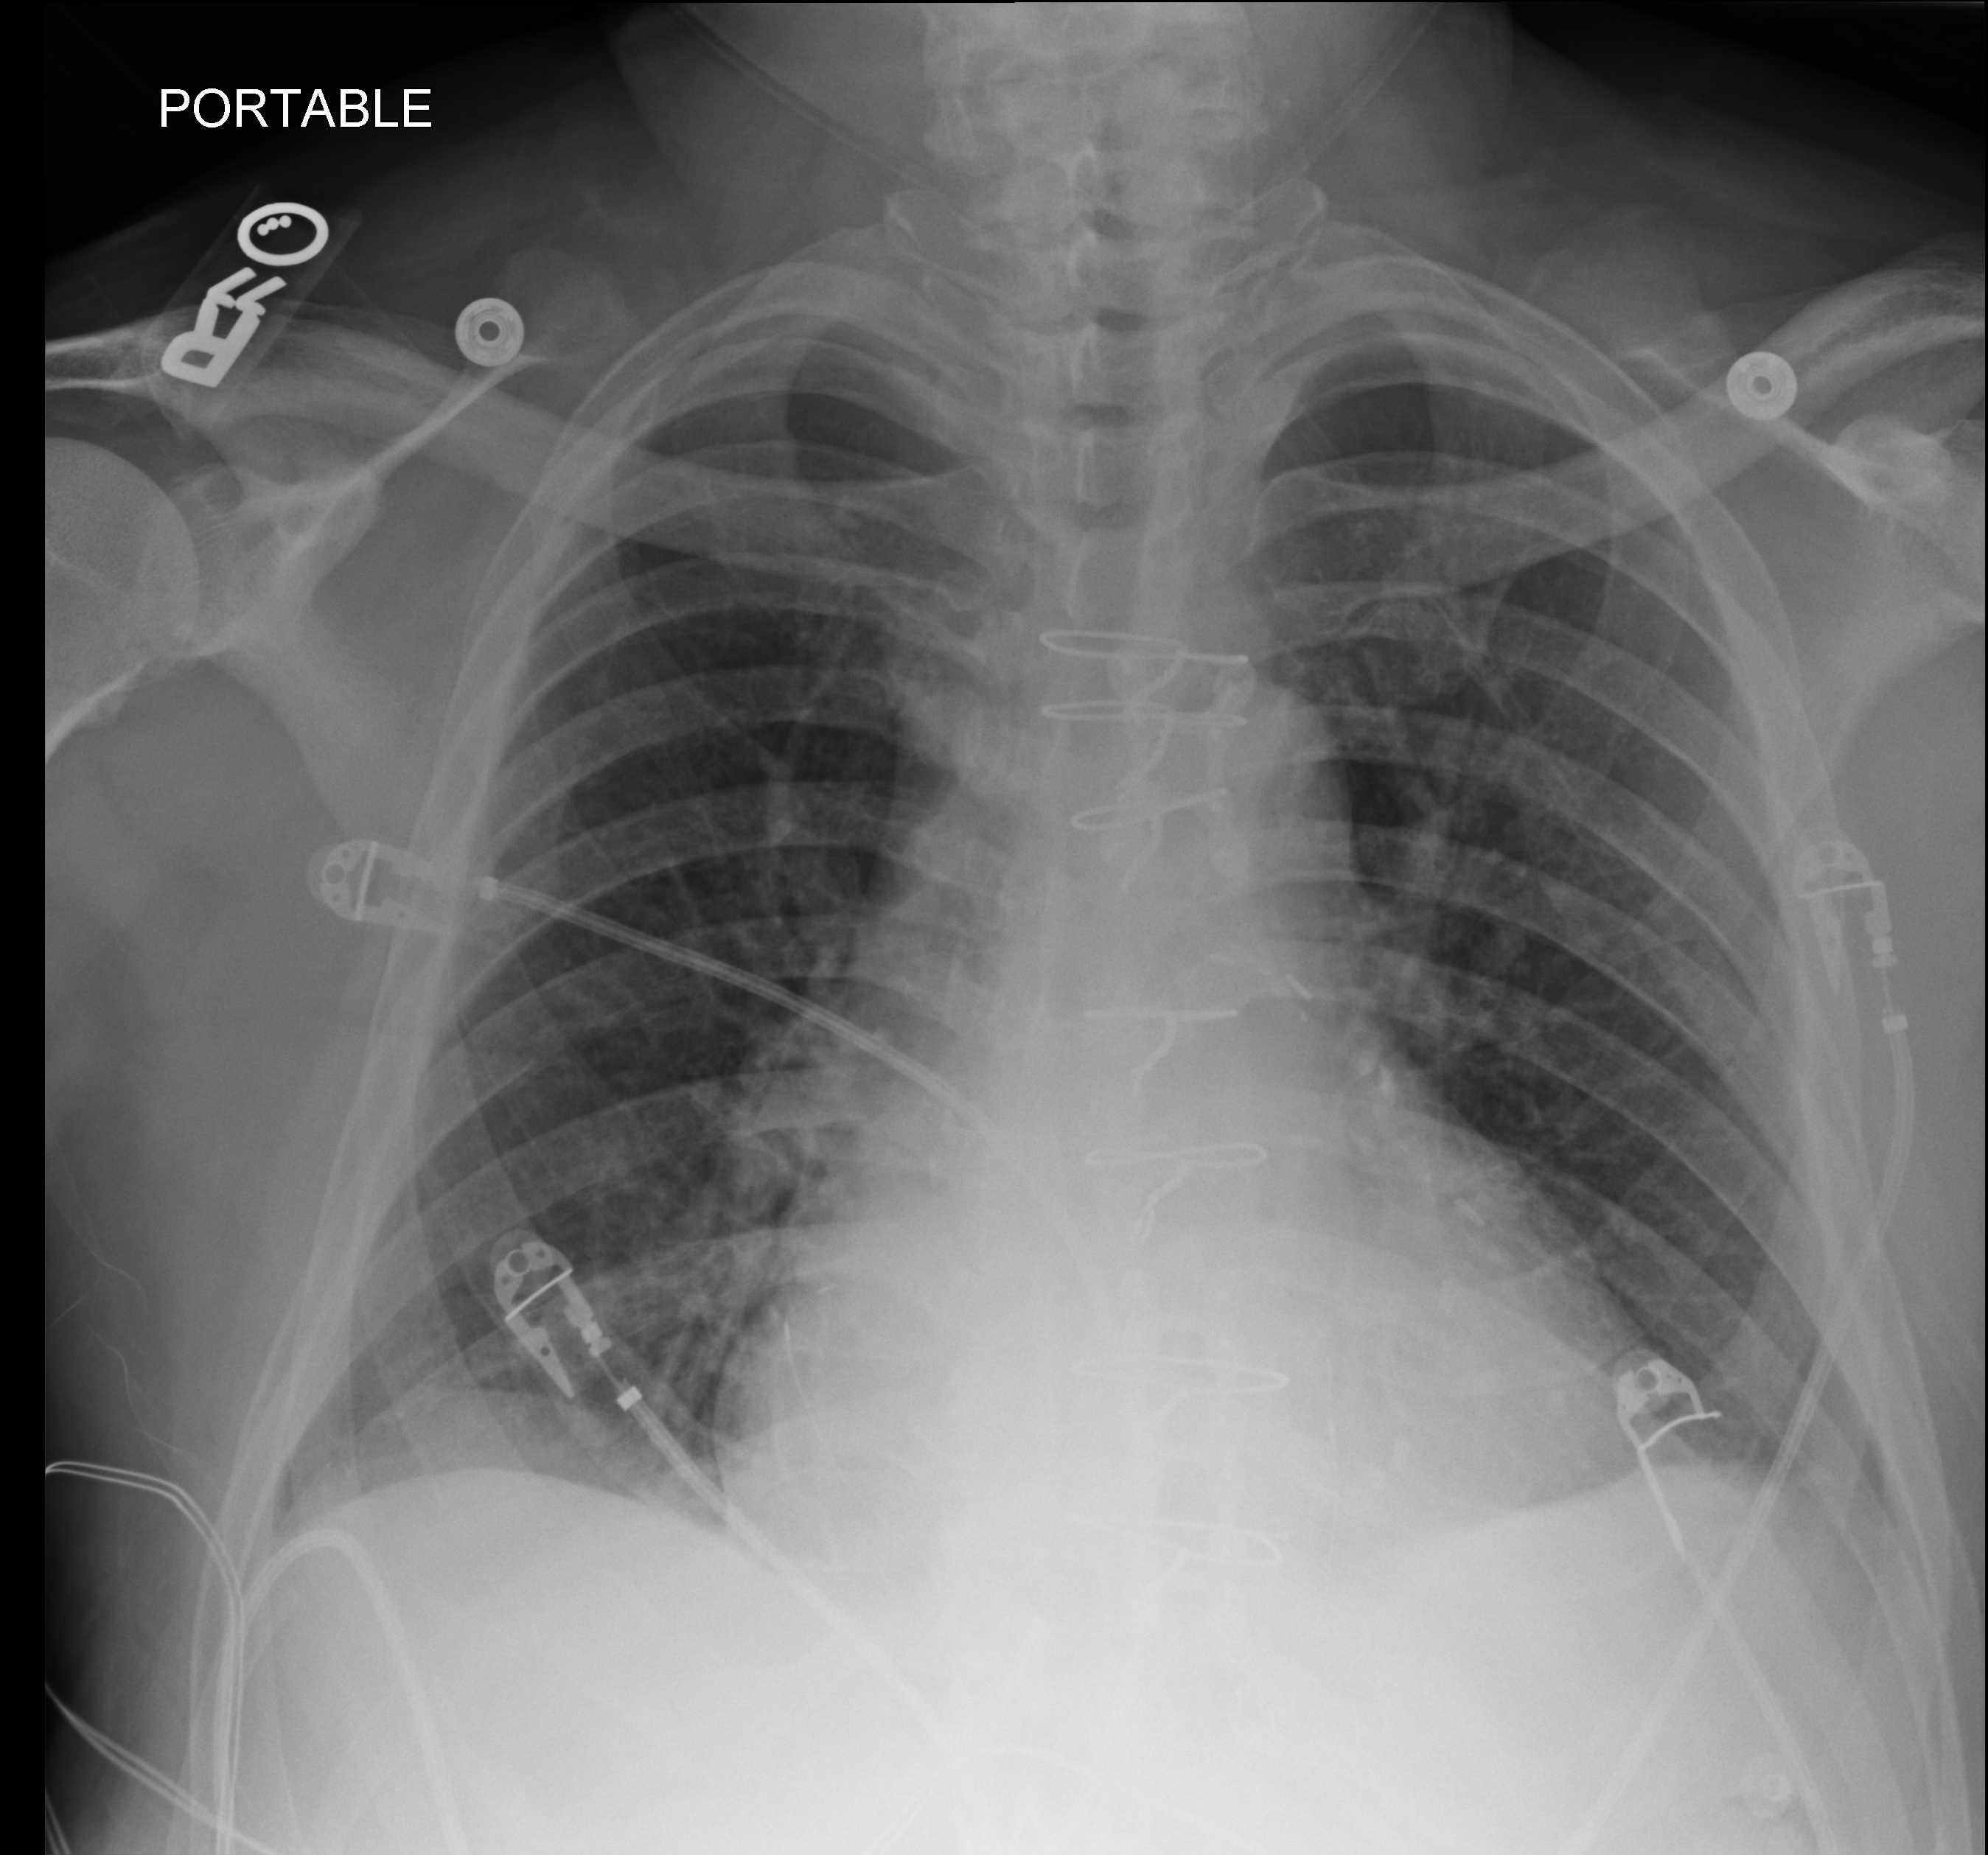
Chest X-ray (portable); anteroposterior (AP) projection. Male patient hospitalised with COVID-19, age 60–74 years.
Admission-level facts for this patient (not findings on this image; timing relative to this image not recorded):
- chronic kidney disease (admission record): no